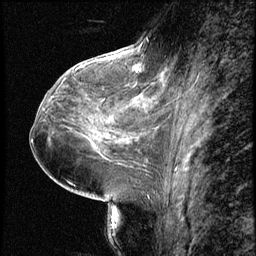
Breast MRI (dynamic contrast-enhanced), one sagittal slice; position 31 of 66 along the scan axis; 3 images stored at this slice position (order not interpretable as contrast timing); 1.5 T; TE 4.2 ms, TR 8.7 ms; 2.5 mm slice thickness; 256 × 256 image matrix, field of view 180 × 180 mm. Patient: female, 38 years. Case-level facts recorded for this patient, not image findings: setting: breast cancer imaged before/during neoadjuvant chemotherapy; receptor status: triple-negative.
Annotated regions visible in this slice (semi-automatically segmented with operator editing):
- analysis volume of interest (the breast-tissue region the enhancement analysis was run in; not a lesion): box from (x=128, y=57) to (x=149, y=78) px
- tumour enhancement mask (voxels above the 140 % enhancement threshold inside the analysis volume of interest): (x=132, y=70)–(x=139, y=71)